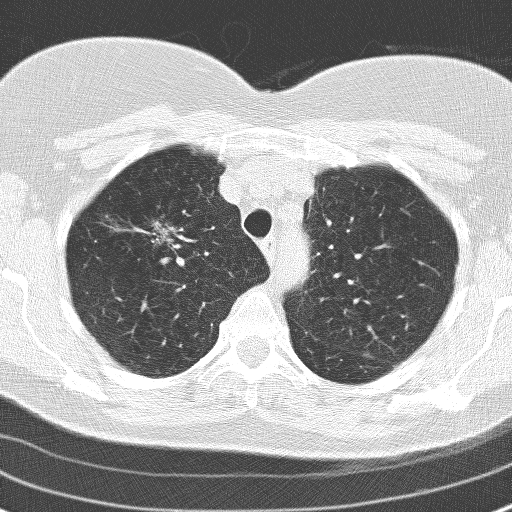
Chest CT (low-dose screening protocol), one axial image. Second annual screen. Lung window (W 1500 / L -600 HU). Female, age 60 years at enrolment. Former smoker at enrolment.
Lesion marked by an expert reader, box from (x=124, y=209) to (x=179, y=257) px. Screening reader's record for this exam (one nodule recorded; not confirmed to be the boxed lesion): non-calcified nodule or mass ≥4 mm, right upper lobe, 17 × 15 mm, spiculated (stellate) margins, soft tissue attenuation, pre-existing on the prior screen: yes; interval growth: yes.